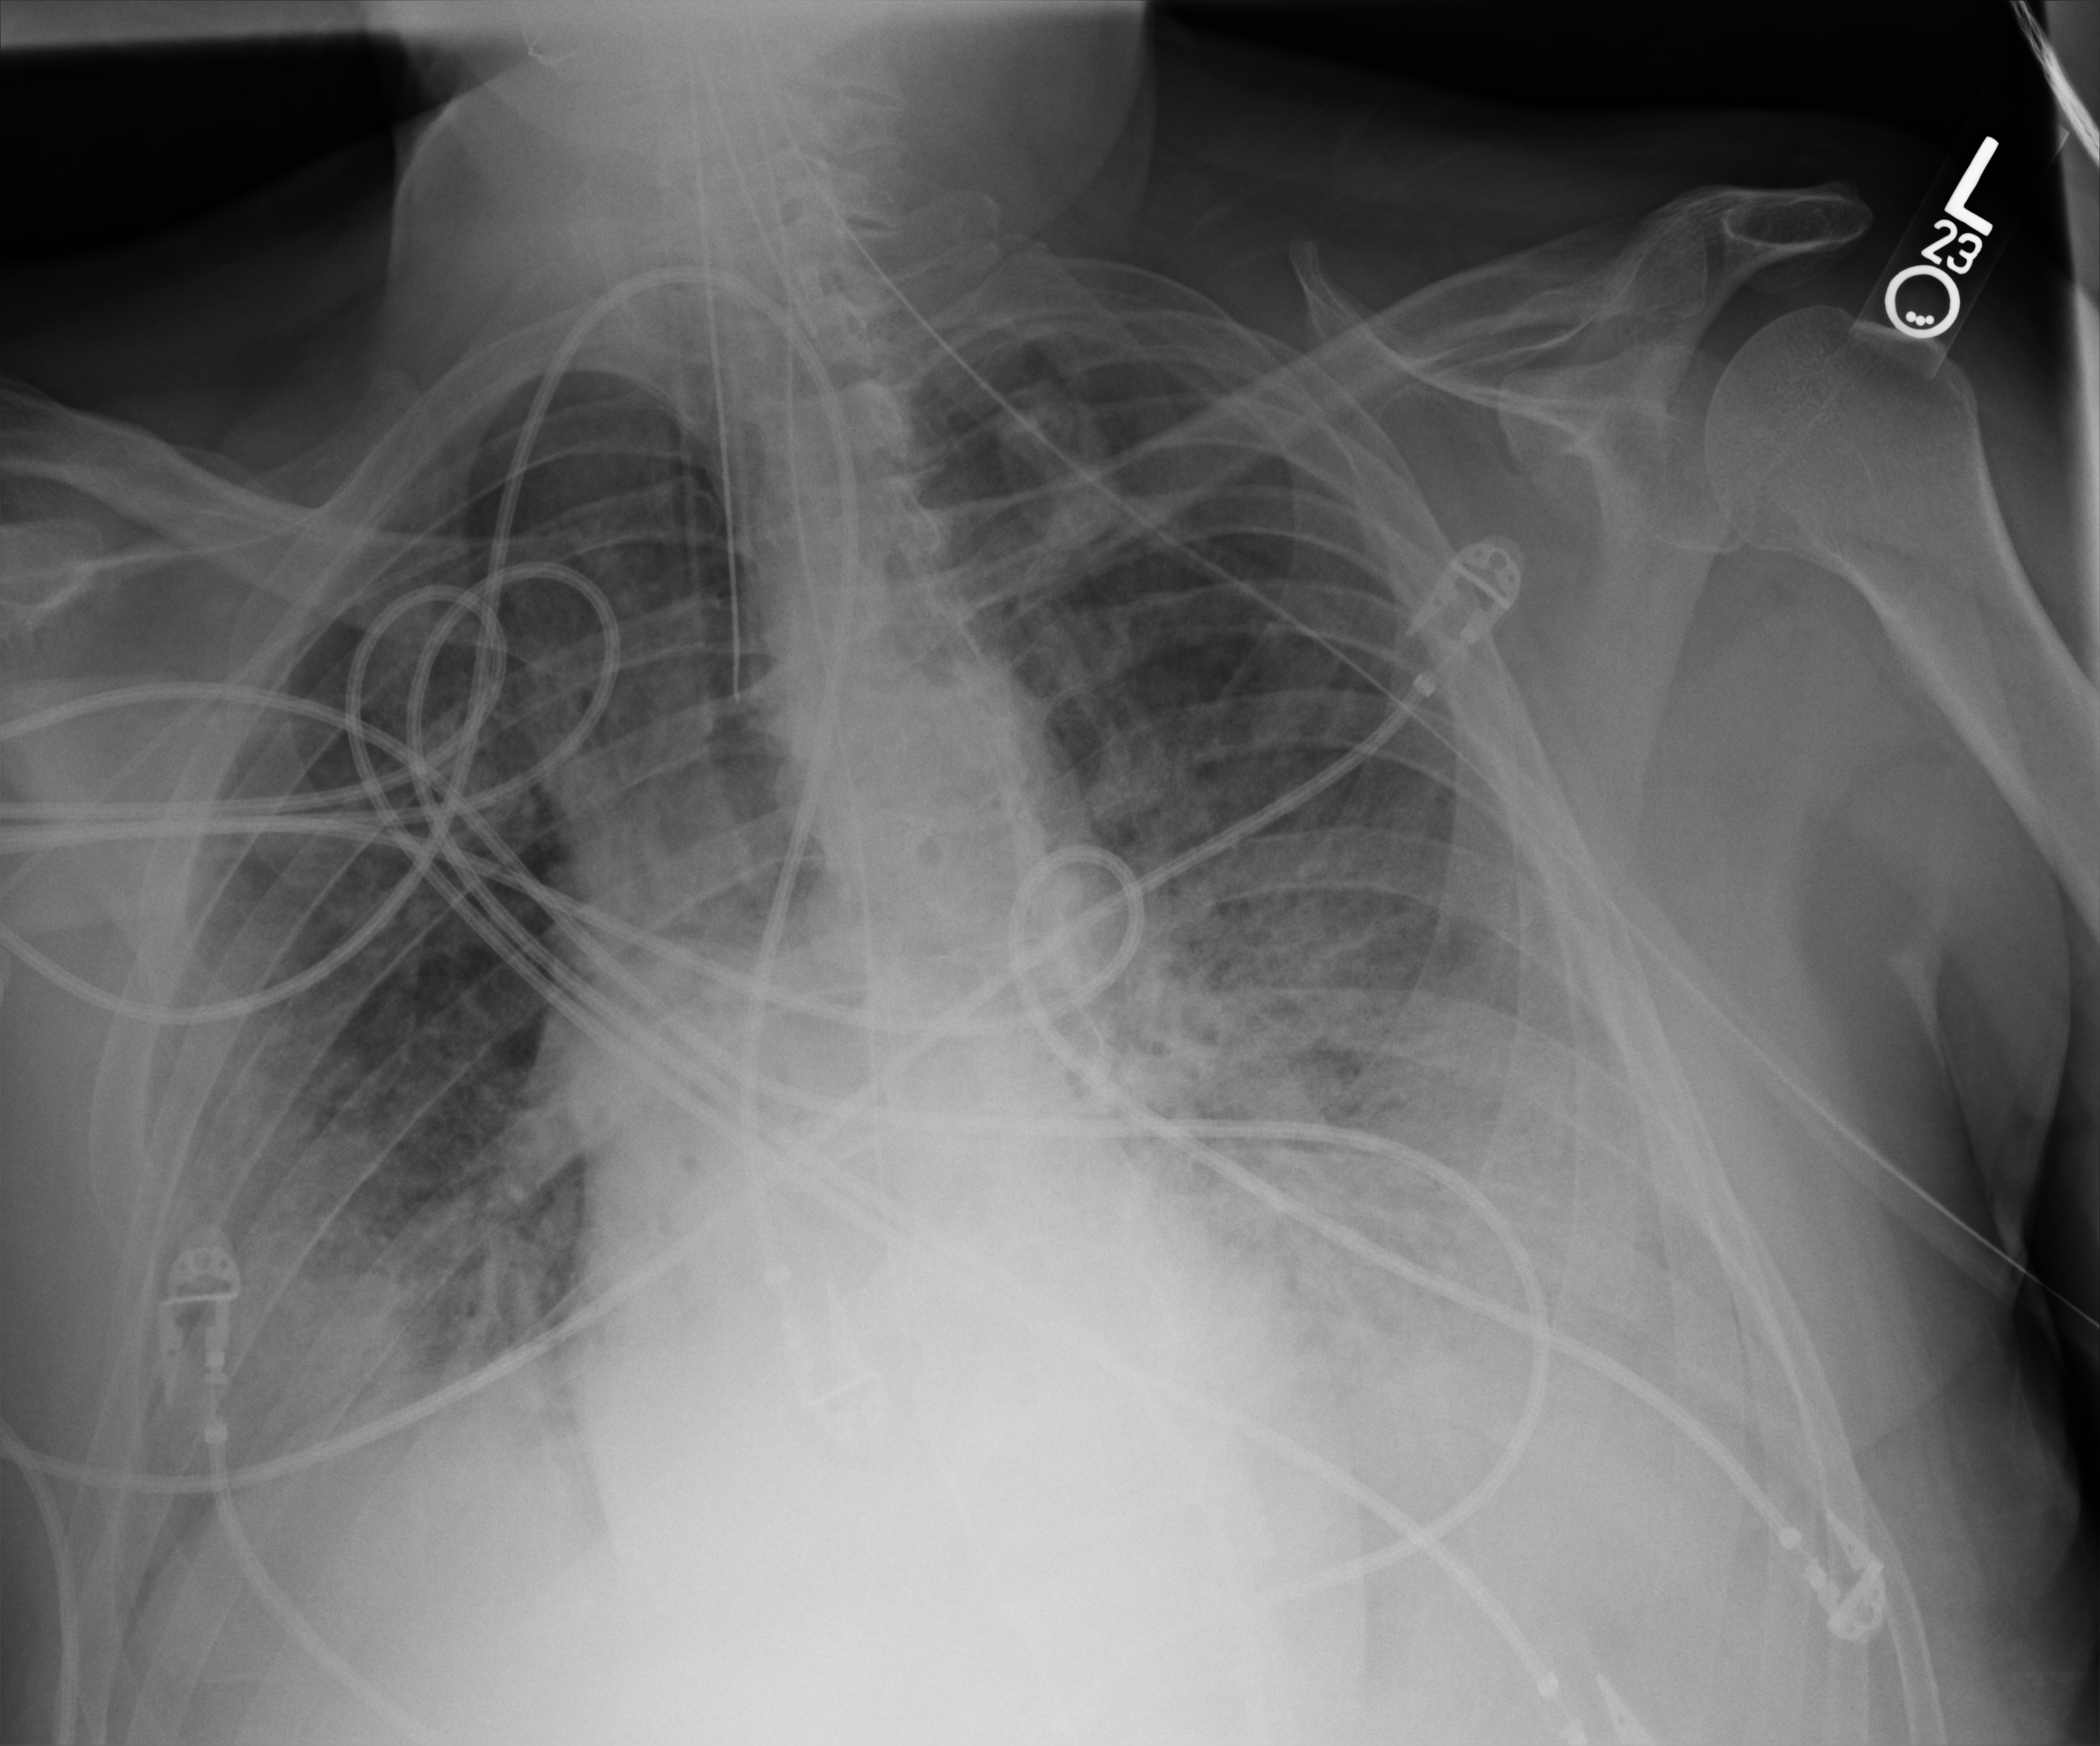
Chest X-ray (portable); anteroposterior (AP) projection. Male patient hospitalised with COVID-19, age 60–74 years.
Admission-level facts for this patient (not findings on this image; timing relative to this image not recorded):
- mechanically ventilated during this hospital stay: yes